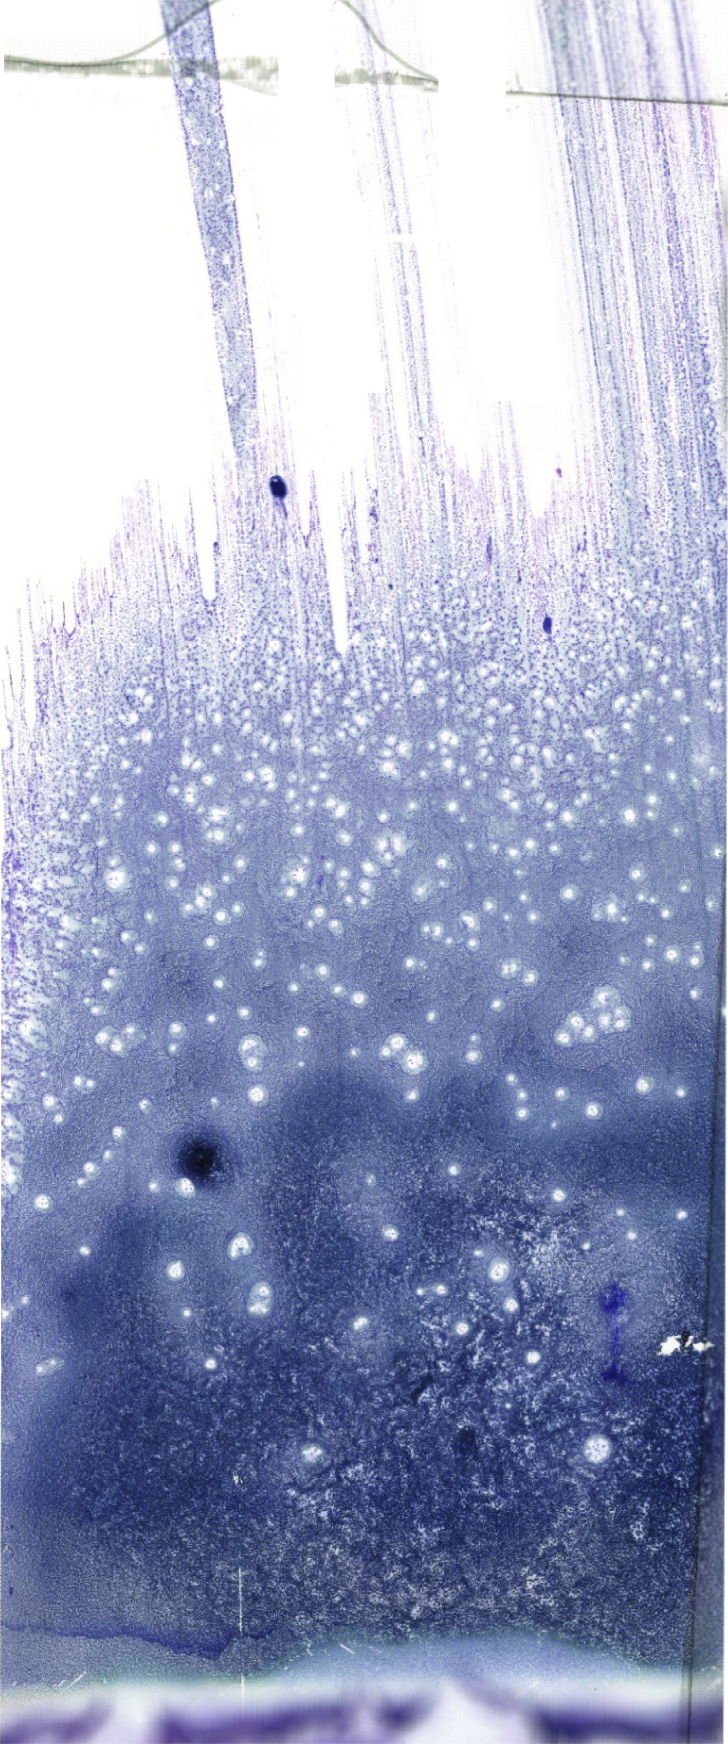
May-Grünwald–Giemsa-stained marrow aspirate smear (whole slide), a low-resolution overview of the entire scanned area, about 20.6 x 49.4 mm. Female patient.
- diagnosis: B Acute Lymphoblastic Leukemia